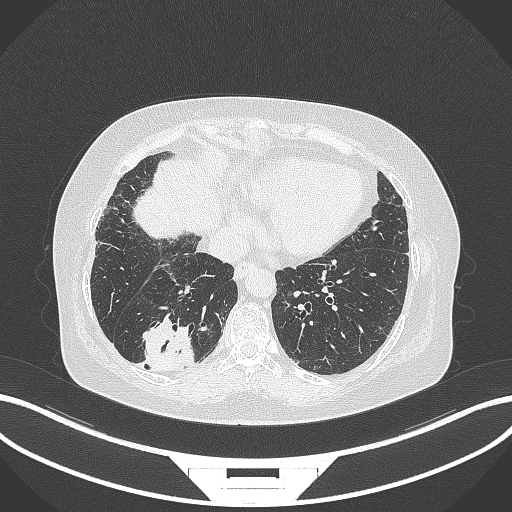
Chest CT, one axial slice. Position 61 of 296 along the scan axis. Reconstruction kernel B70f. 120 kVp. Lung window (W 1500 / L -600 HU). 1 mm slice thickness. 512 × 512 image matrix, field of view 400 × 400 mm. Female patient, age 65 years. Case-level facts recorded for this patient, not image findings: clinical TNM (as recorded): T2b N1 M0; histopathological grade: G1.
Outlined on this slice (rectangle marked by the reading radiologist):
- lung tumour (recorded histology: adenocarcinoma): bounding box (x1, y1, x2, y2) in pixels: (138, 314, 200, 373)